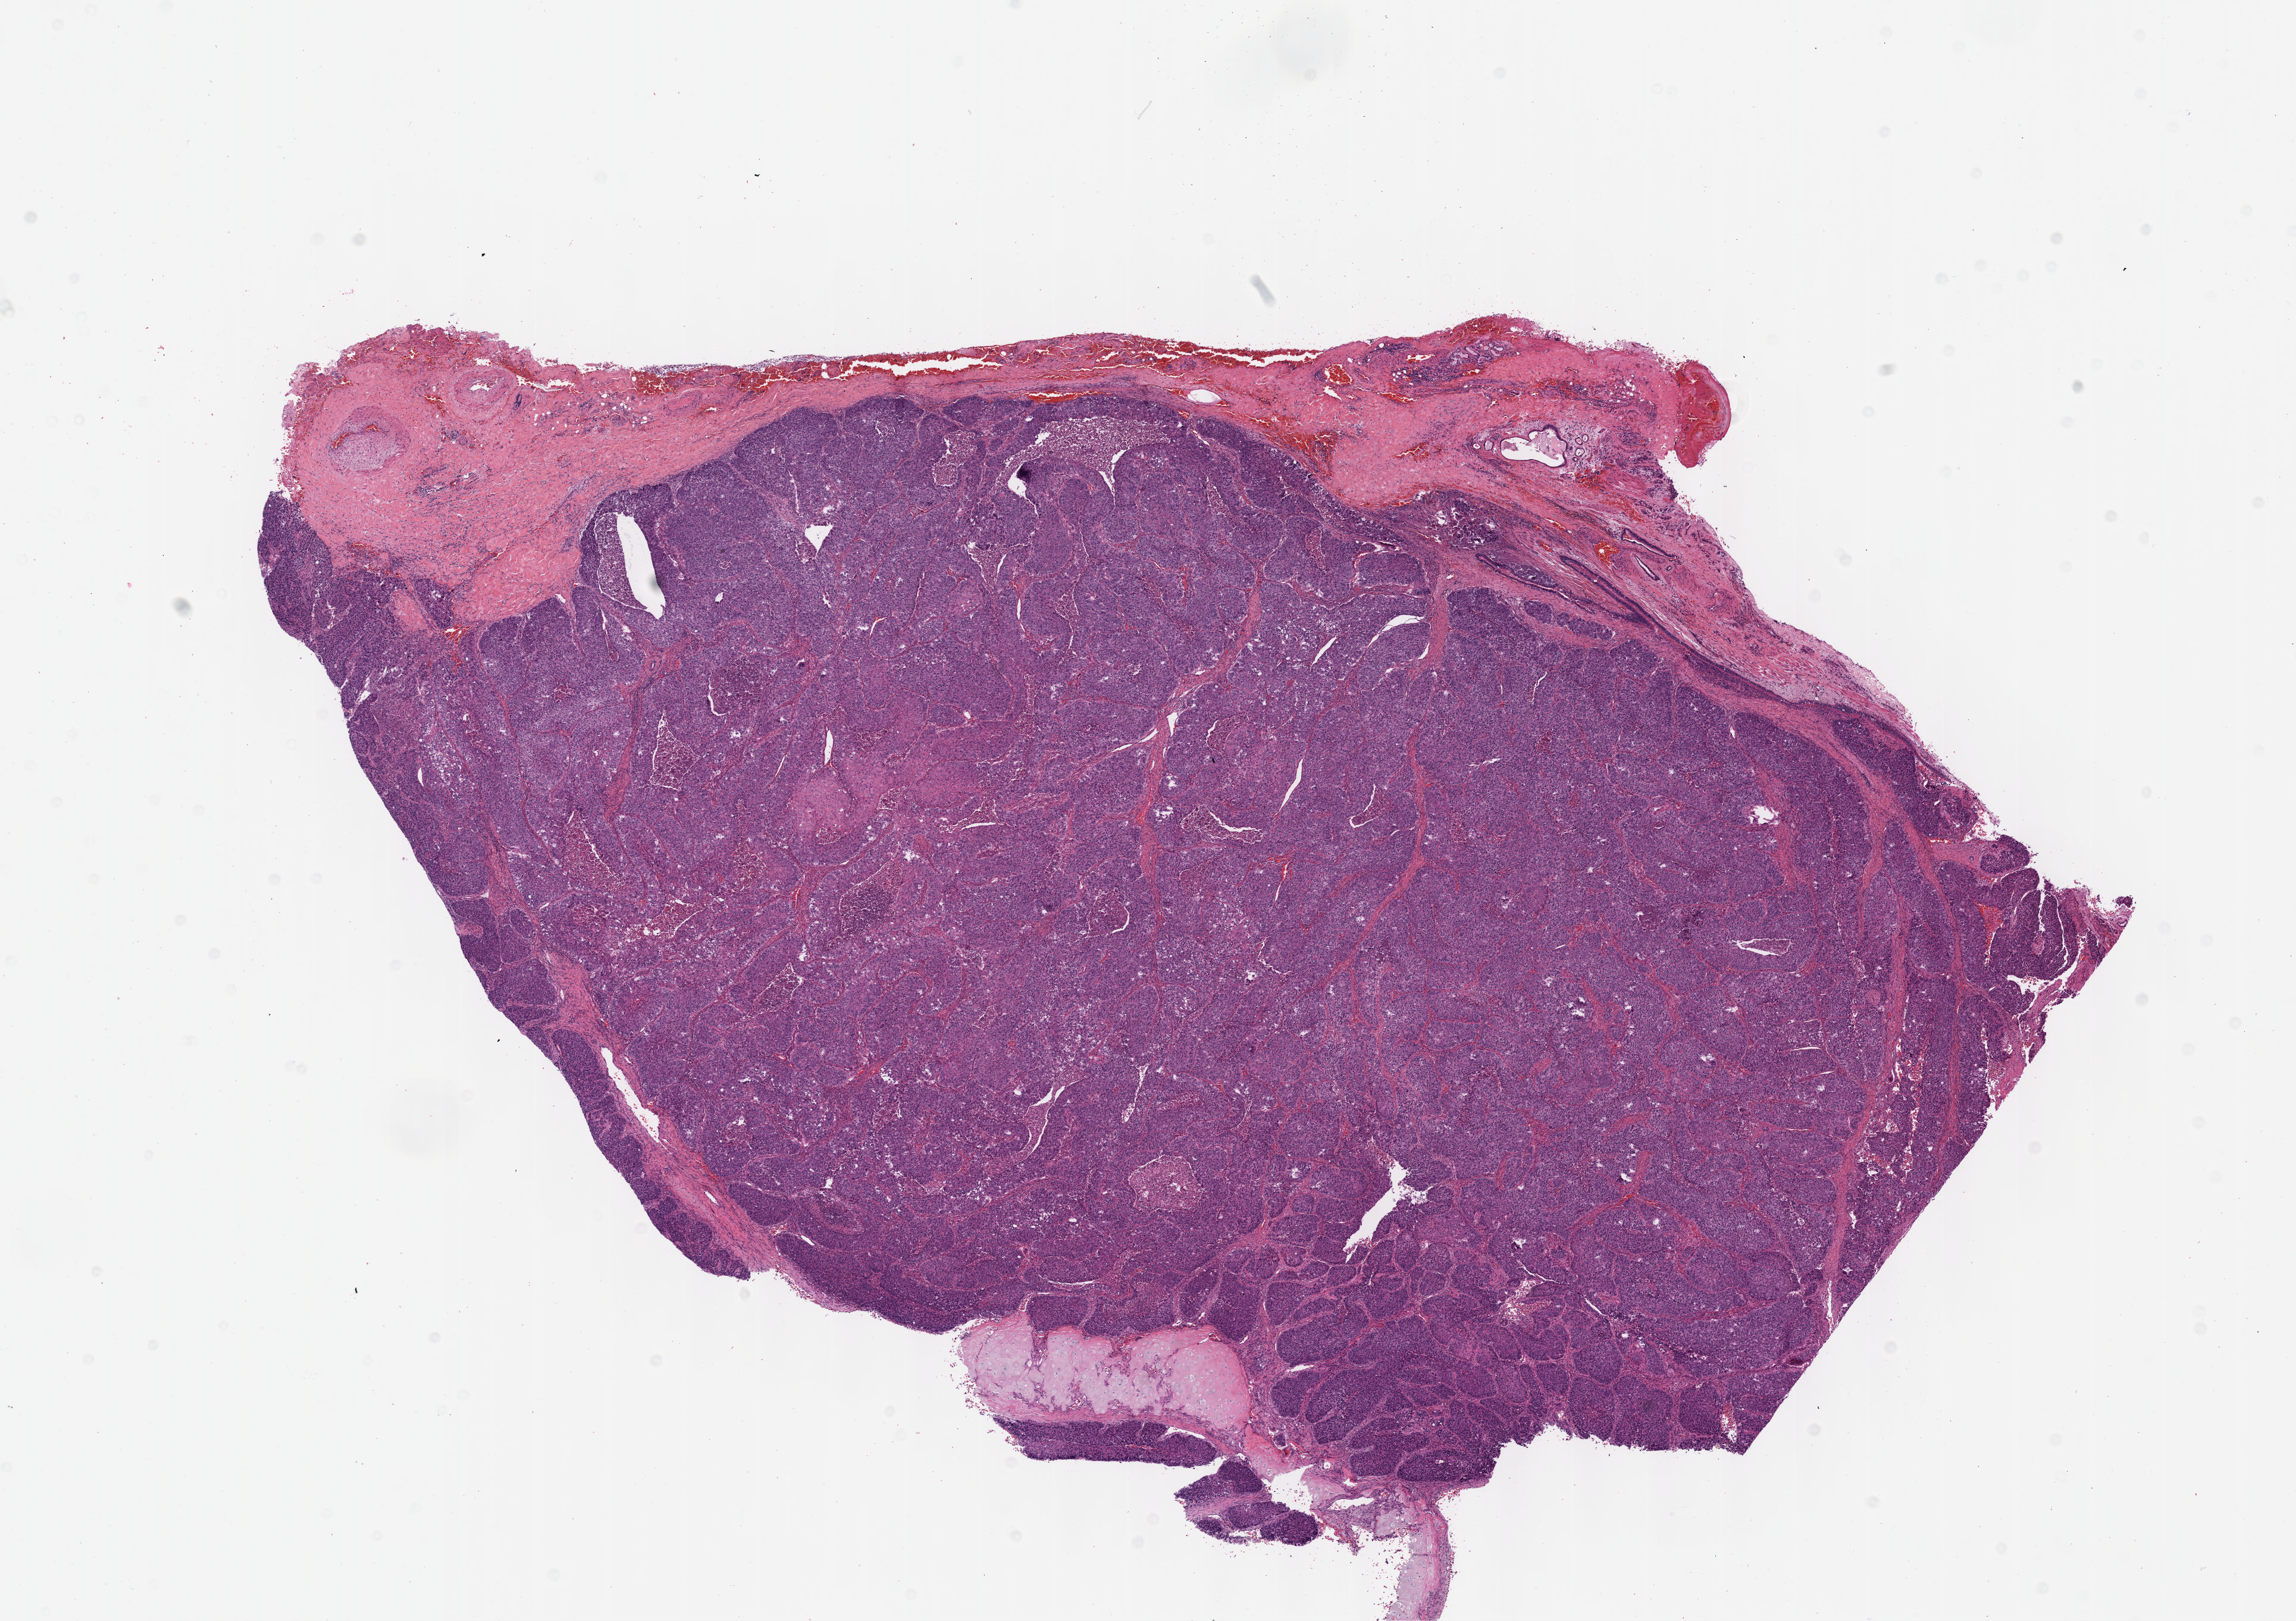
Whole-slide histology image, Hematoxylin and eosin (H&E) stained, a low-resolution overview of the entire scanned area, about 15.6 x 11.0 mm; formalin-fixed paraffin-embedded (FFPE) diagnostic section; primary tumour sample from the lung. Male, age 53 years at initial diagnosis.
* AJCC pathologic stage: IIB (7th edition)
* laterality: left
* pathologic diagnosis: Squamous cell carcinoma, NOS (upper lobe, lung)